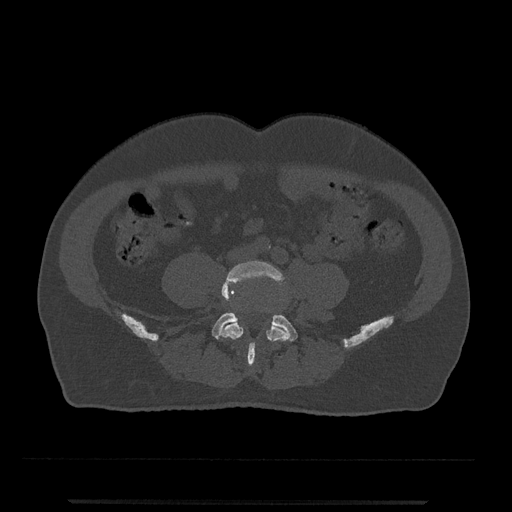
CT including the spine, one axial slice; slice 103 of 797 in the series (ordered by position); reconstruction kernel Br40s/3; bone window (W 1800 / L 400 HU); 0.5 mm slice thickness; 512 × 512 image matrix, field of view 419 × 419 mm. Male patient, age 63 years. Case-level facts recorded for this patient, not image findings: primary cancer: prostate.
Structures marked on this image (semi-automatic segmentation, software-assisted and operator-edited):
- L4 vertebra: box from (x=221, y=261) to (x=290, y=366) px
- L5 vertebra: (x=212, y=312)–(x=298, y=360)